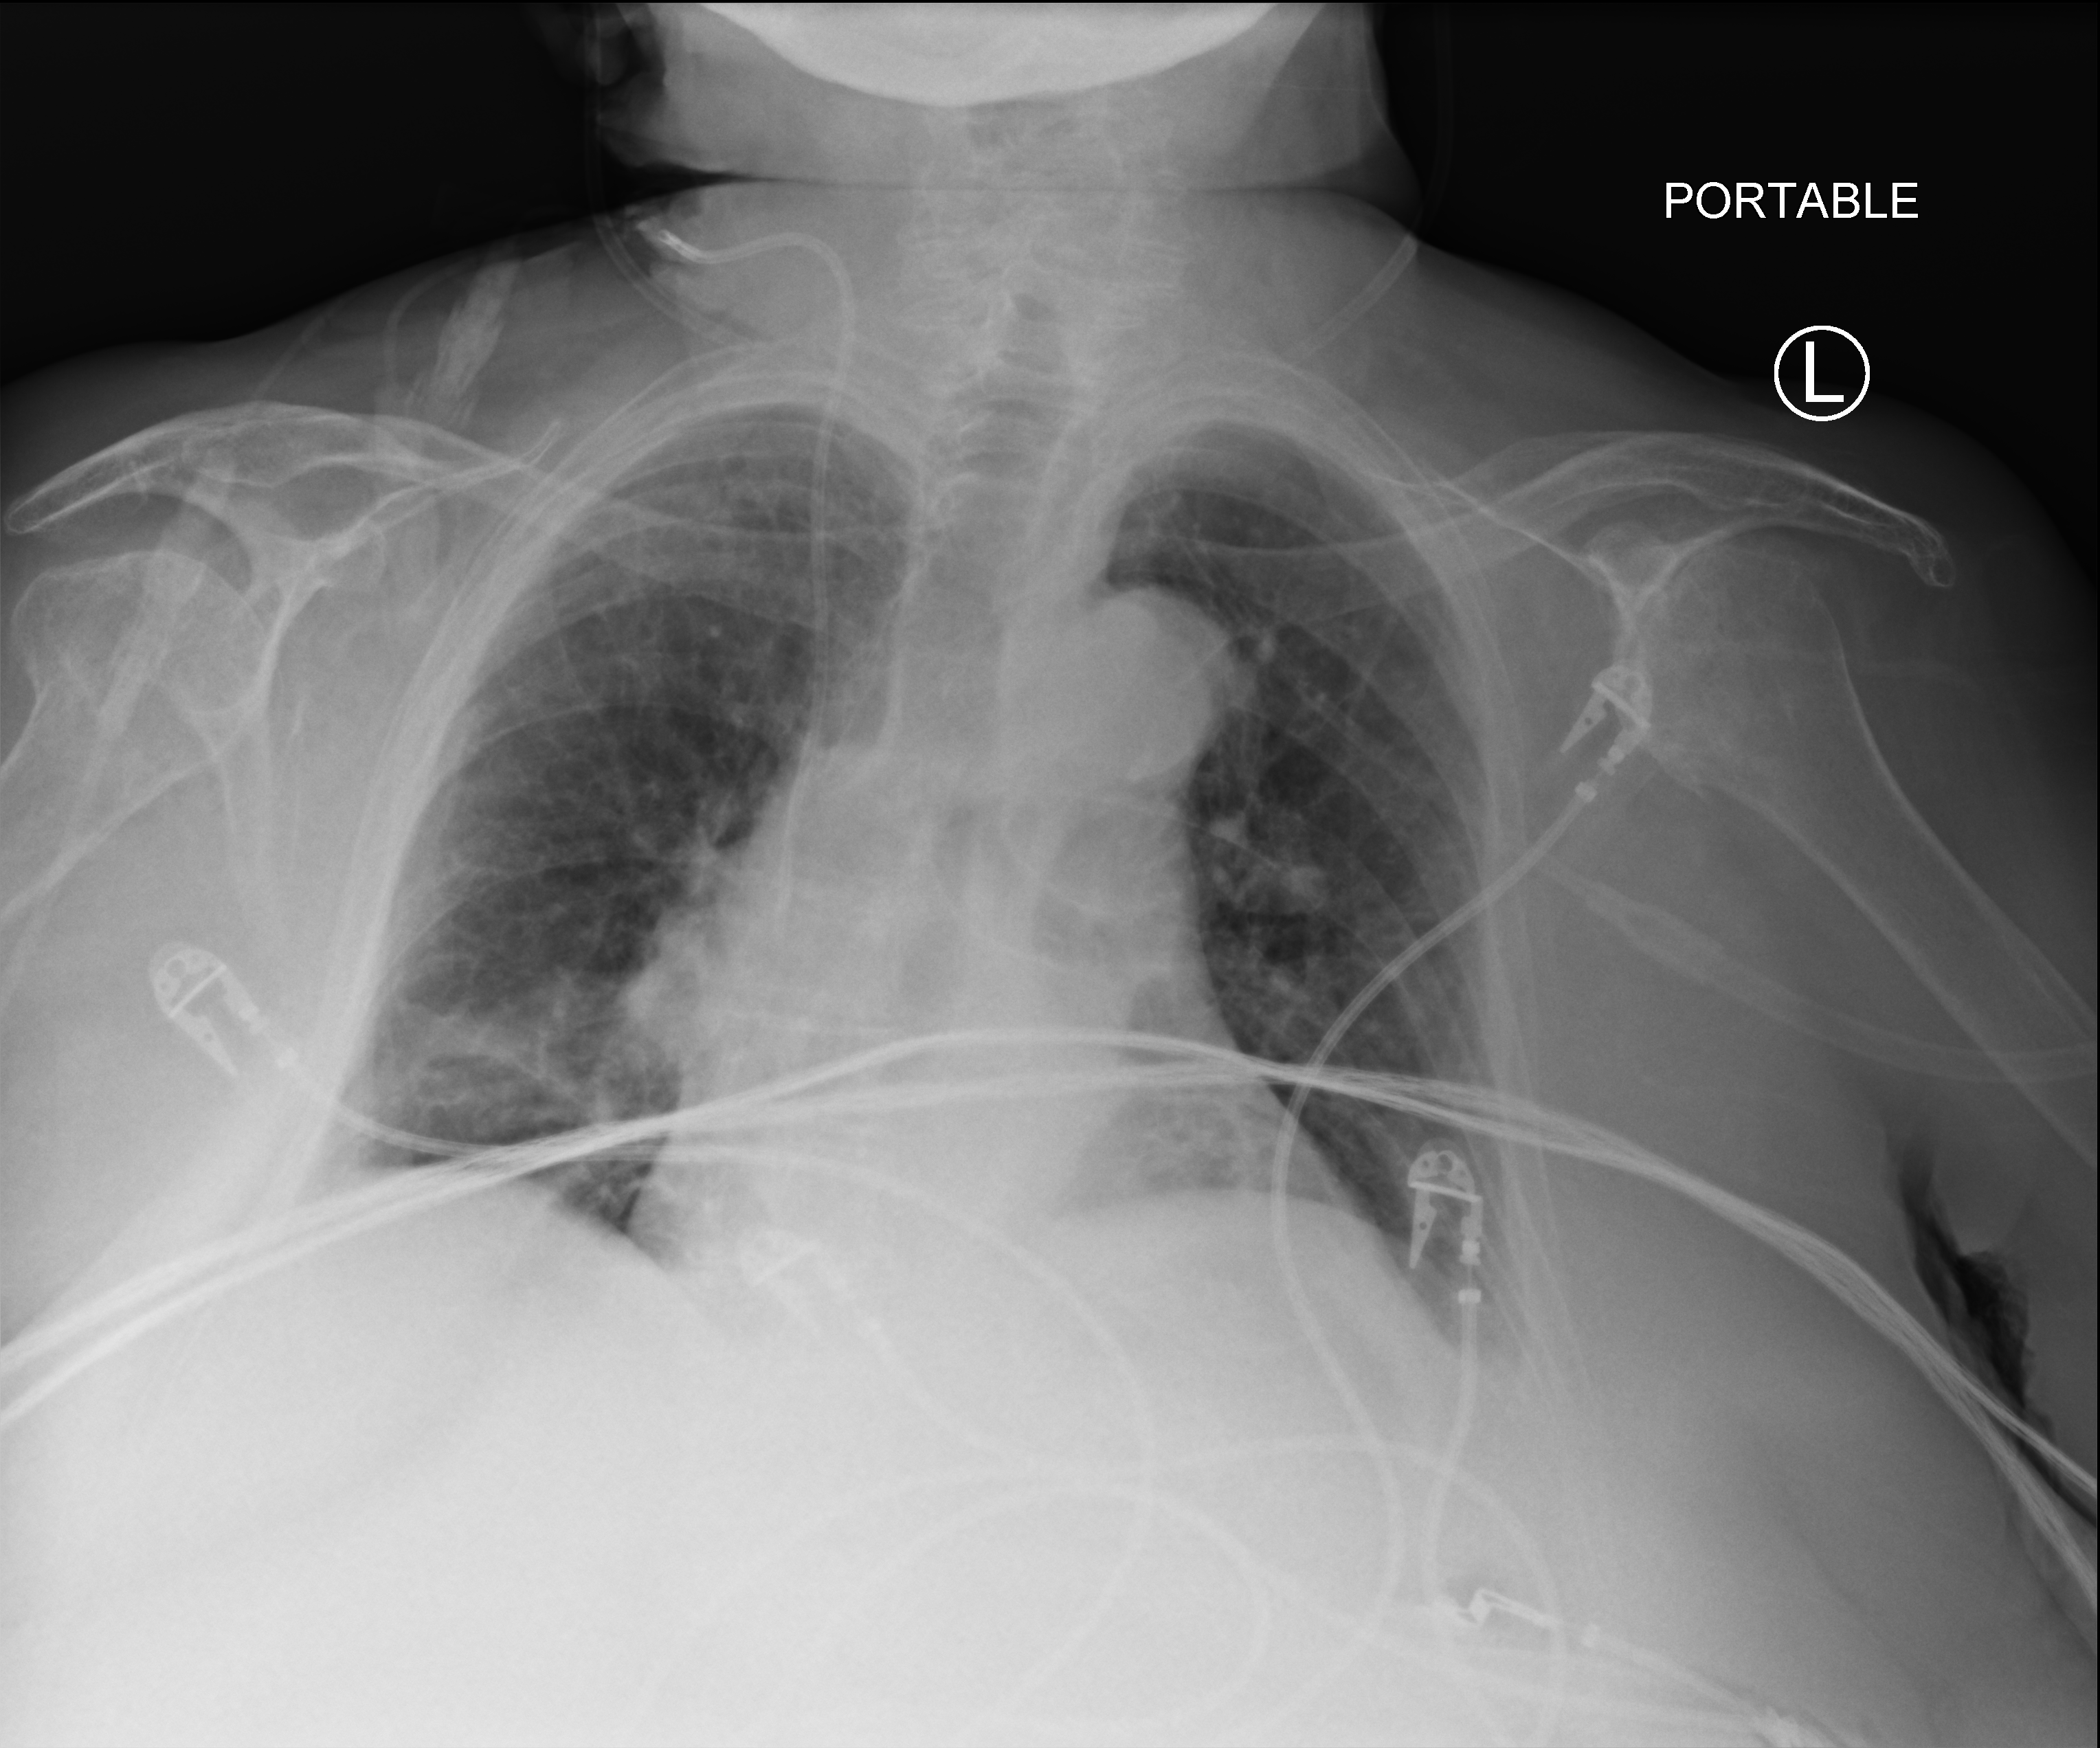
Chest X-ray (portable); anteroposterior (AP) projection. Female patient hospitalised with COVID-19, age 75–90 years.
Hospital-stay facts (about this admission, not read from this image; timing relative to this image not recorded):
- mechanically ventilated during this hospital stay: no